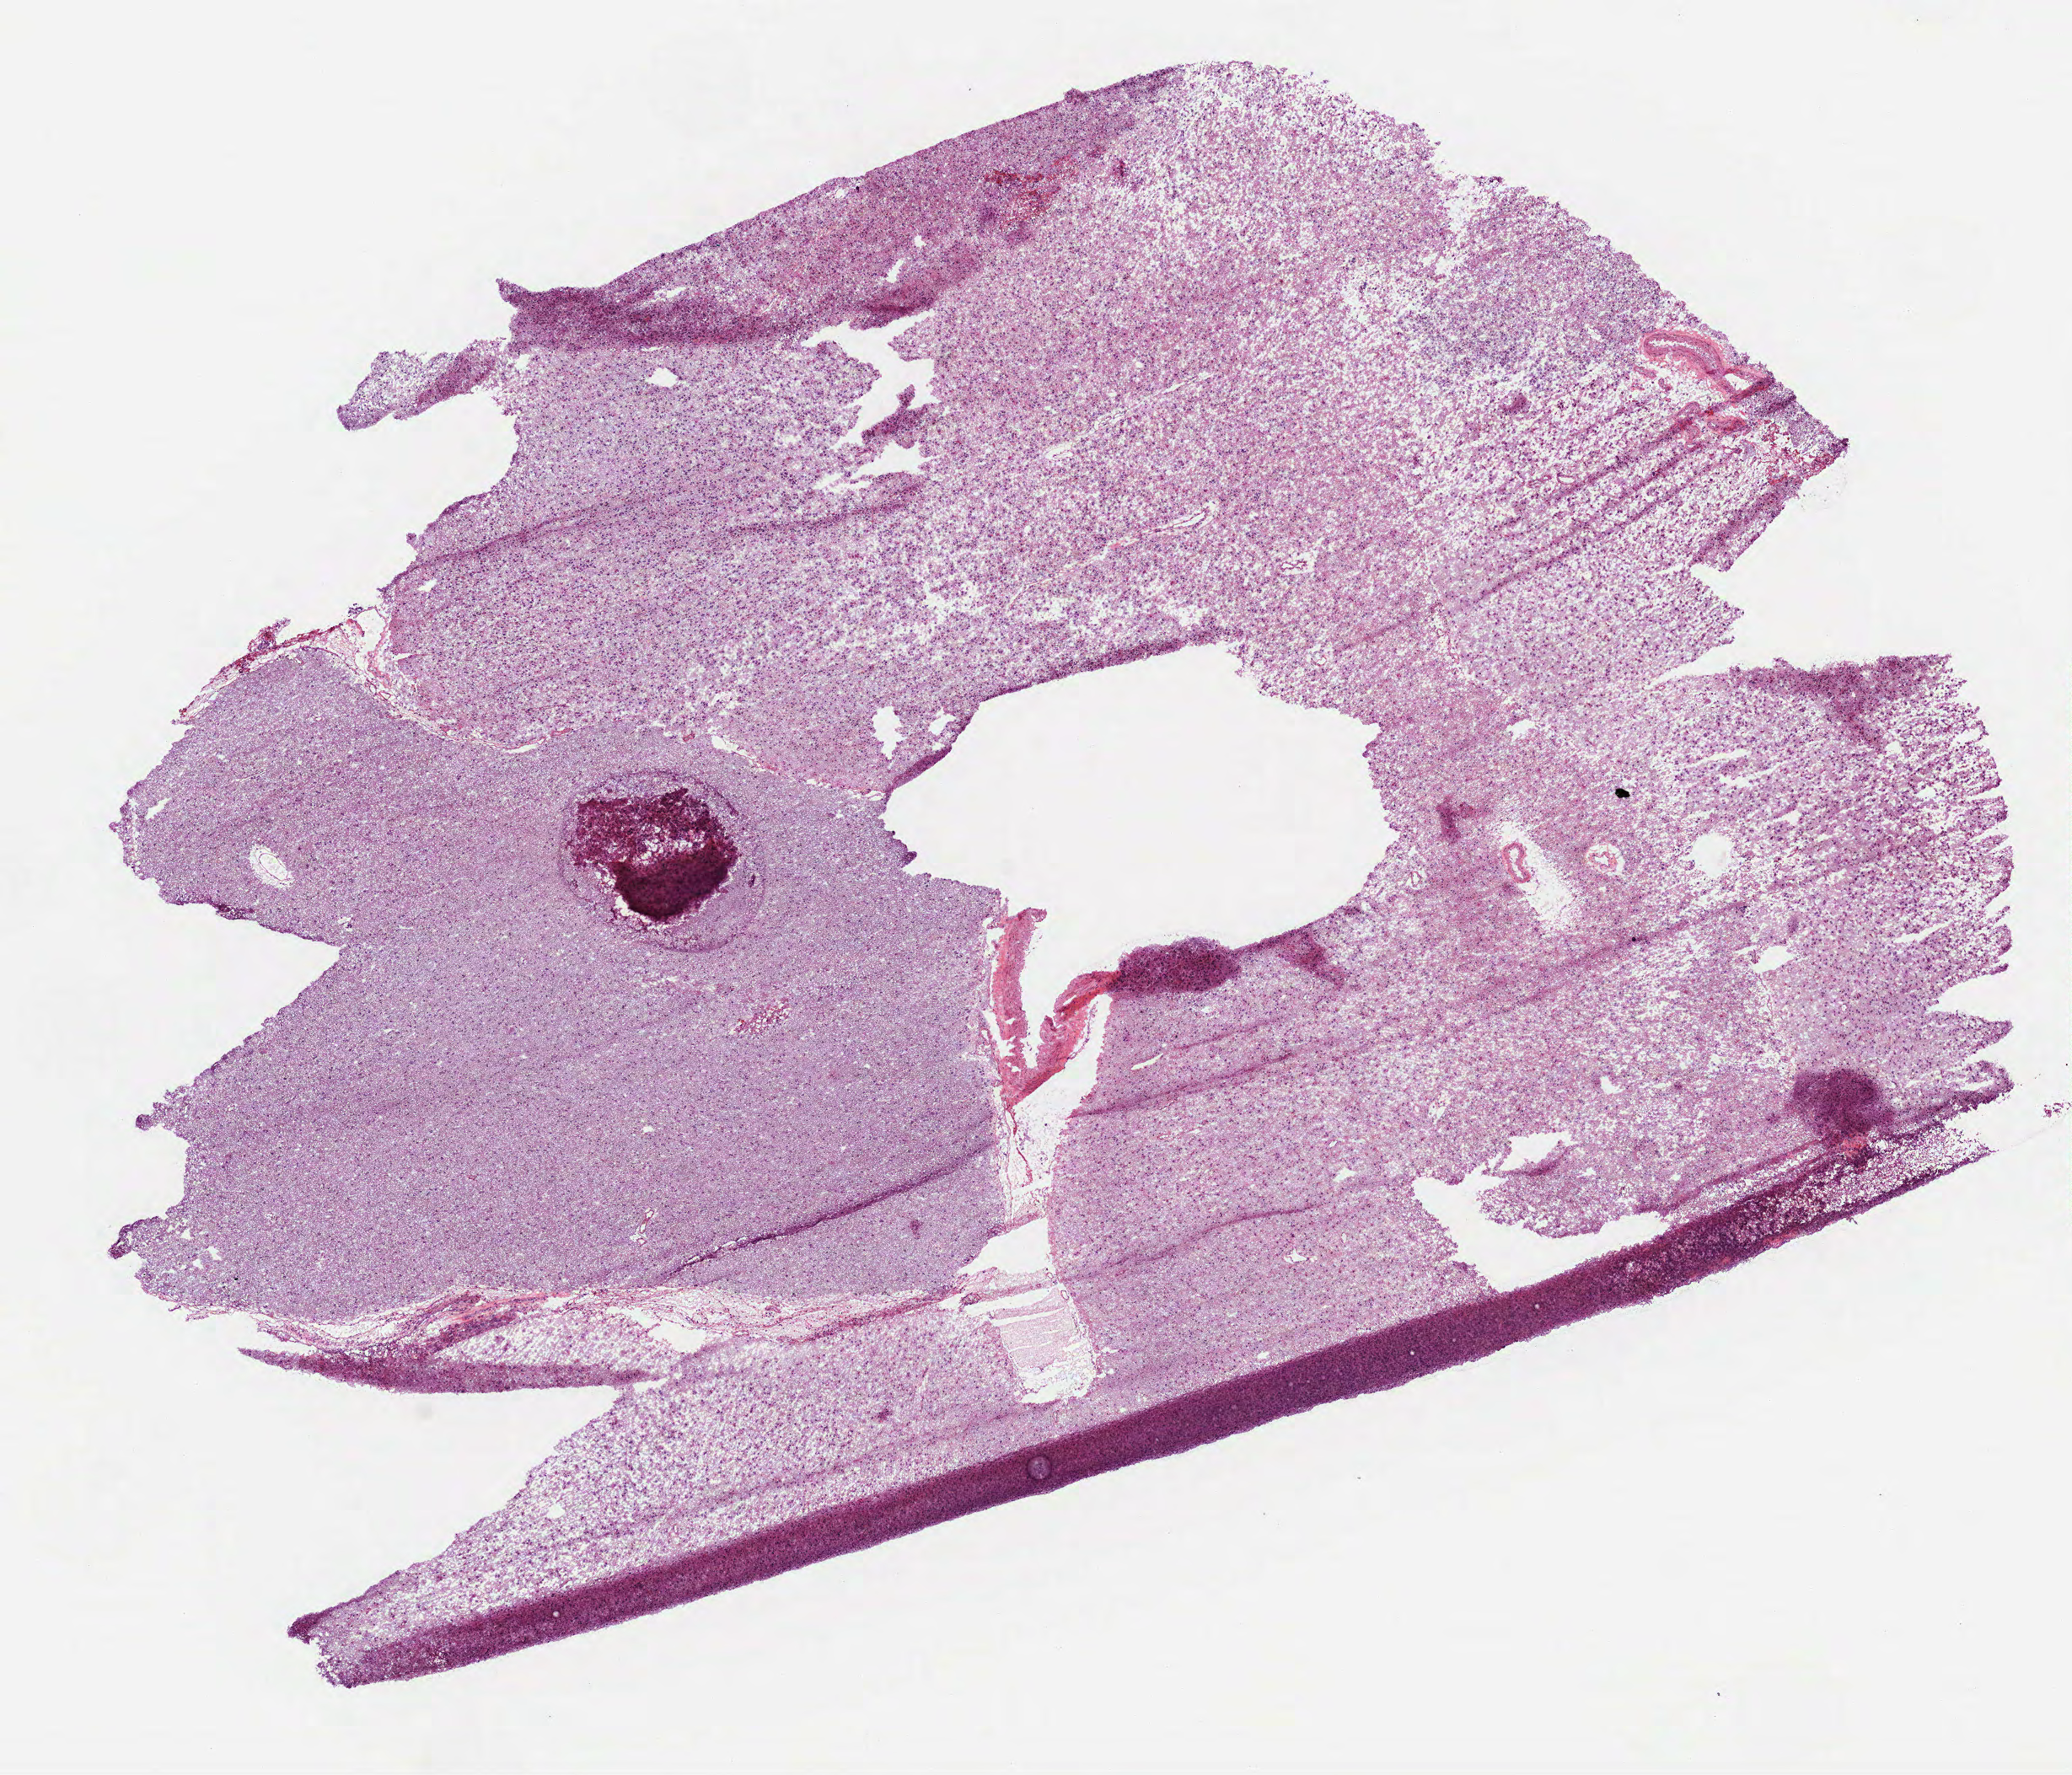
H&E whole-slide image — shown as a low-resolution overview of the whole scanned area (about 9.9 x 8.5 mm, from a 40x scan). Frozen section. Brain, primary tumour sample. Female, age 53 years at initial diagnosis. Histologic grade: G3 (poorly differentiated). Pathologist review of this section (percent, as recorded): tumour cells 100%, tumour nuclei 60%, normal cells 0%, stromal cells 0%, necrosis 0%.
- diagnosis: Oligodendroglioma, anaplastic (cerebrum)